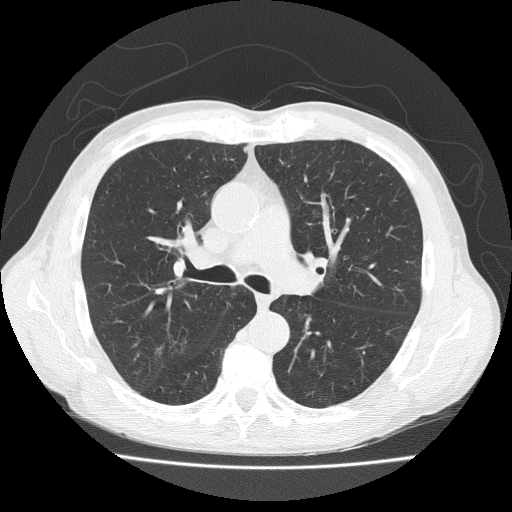
Axial slice from a low-dose chest CT screening exam. Baseline annual screen. Lung window (W 1500 / L -600 HU). 2 mm slice thickness. Lung (sharp) reconstruction kernel (FC51). 120 kVp. Slice 79 of 203 in the series. Male participant, aged 73 years at enrolment. Current smoker at enrolment.
Expert reader's lesion annotation, box from (x=143, y=326) to (x=190, y=372) px. Screening reader's record for this exam: no non-calcified nodule ≥4 mm recorded. Later outcome: lung cancer diagnosed 777 days after this screen (after the third annual screen) — adenosquamous carcinoma, right upper lobe, well differentiated (G1), stage IA (AJCC 6th edition), 20 mm at pathology.